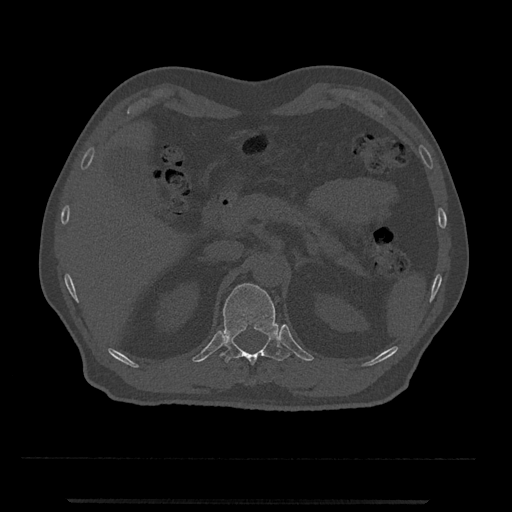
CT including the spine, one axial slice; slice 406 of 797 in the series (ordered by position); reconstruction kernel Br40s/3; 120 kVp; bone window (W 1800 / L 400 HU); 512 × 512 image matrix, field of view 419 × 419 mm. Patient: male, 63 years. Case-level facts recorded for this patient, not image findings: primary cancer: prostate.
Annotated regions visible in this slice (semi-automatic segmentation, software-assisted and operator-edited):
- T12 vertebra: bounding box <220,283,290,365> (left, top, right, bottom; pixels)